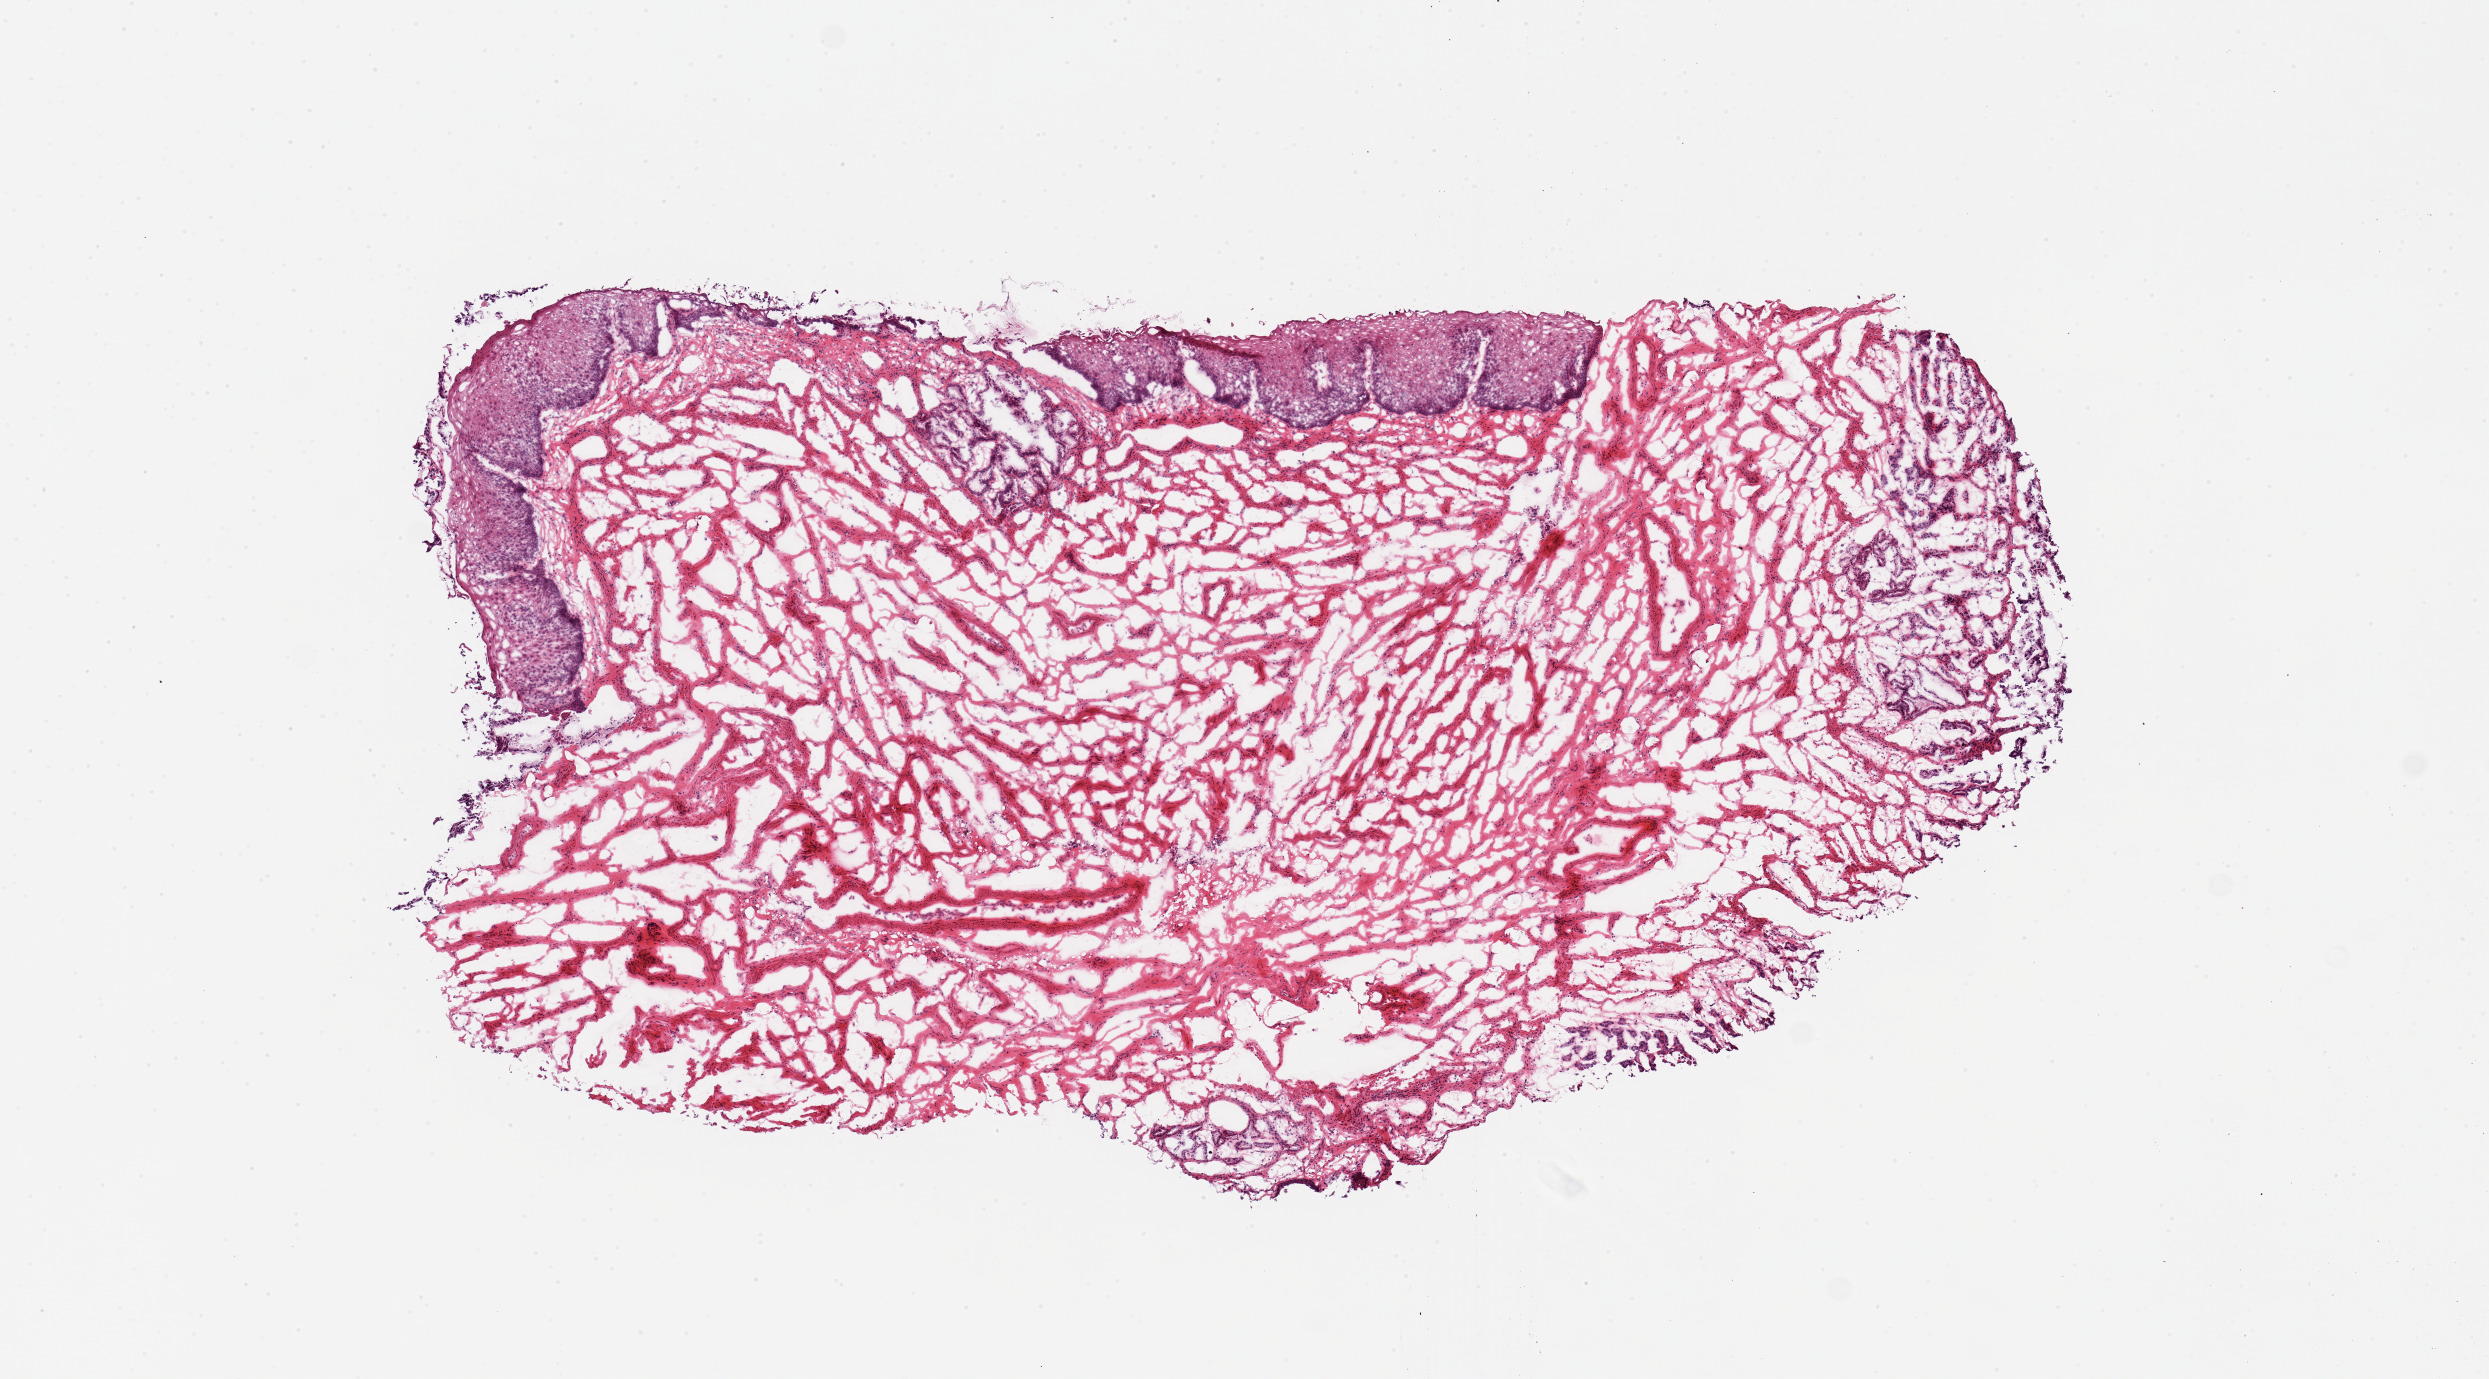
Digitized H&E-stained section — a low-resolution overview of the entire scanned area, about 9.8 x 5.5 mm (from a 20x scan); frozen section; section of esophageal mucous membrane (target tissue); tissue donor sample. Female donor.
Review note (as recorded): 1 piece, consistent with GE junction.